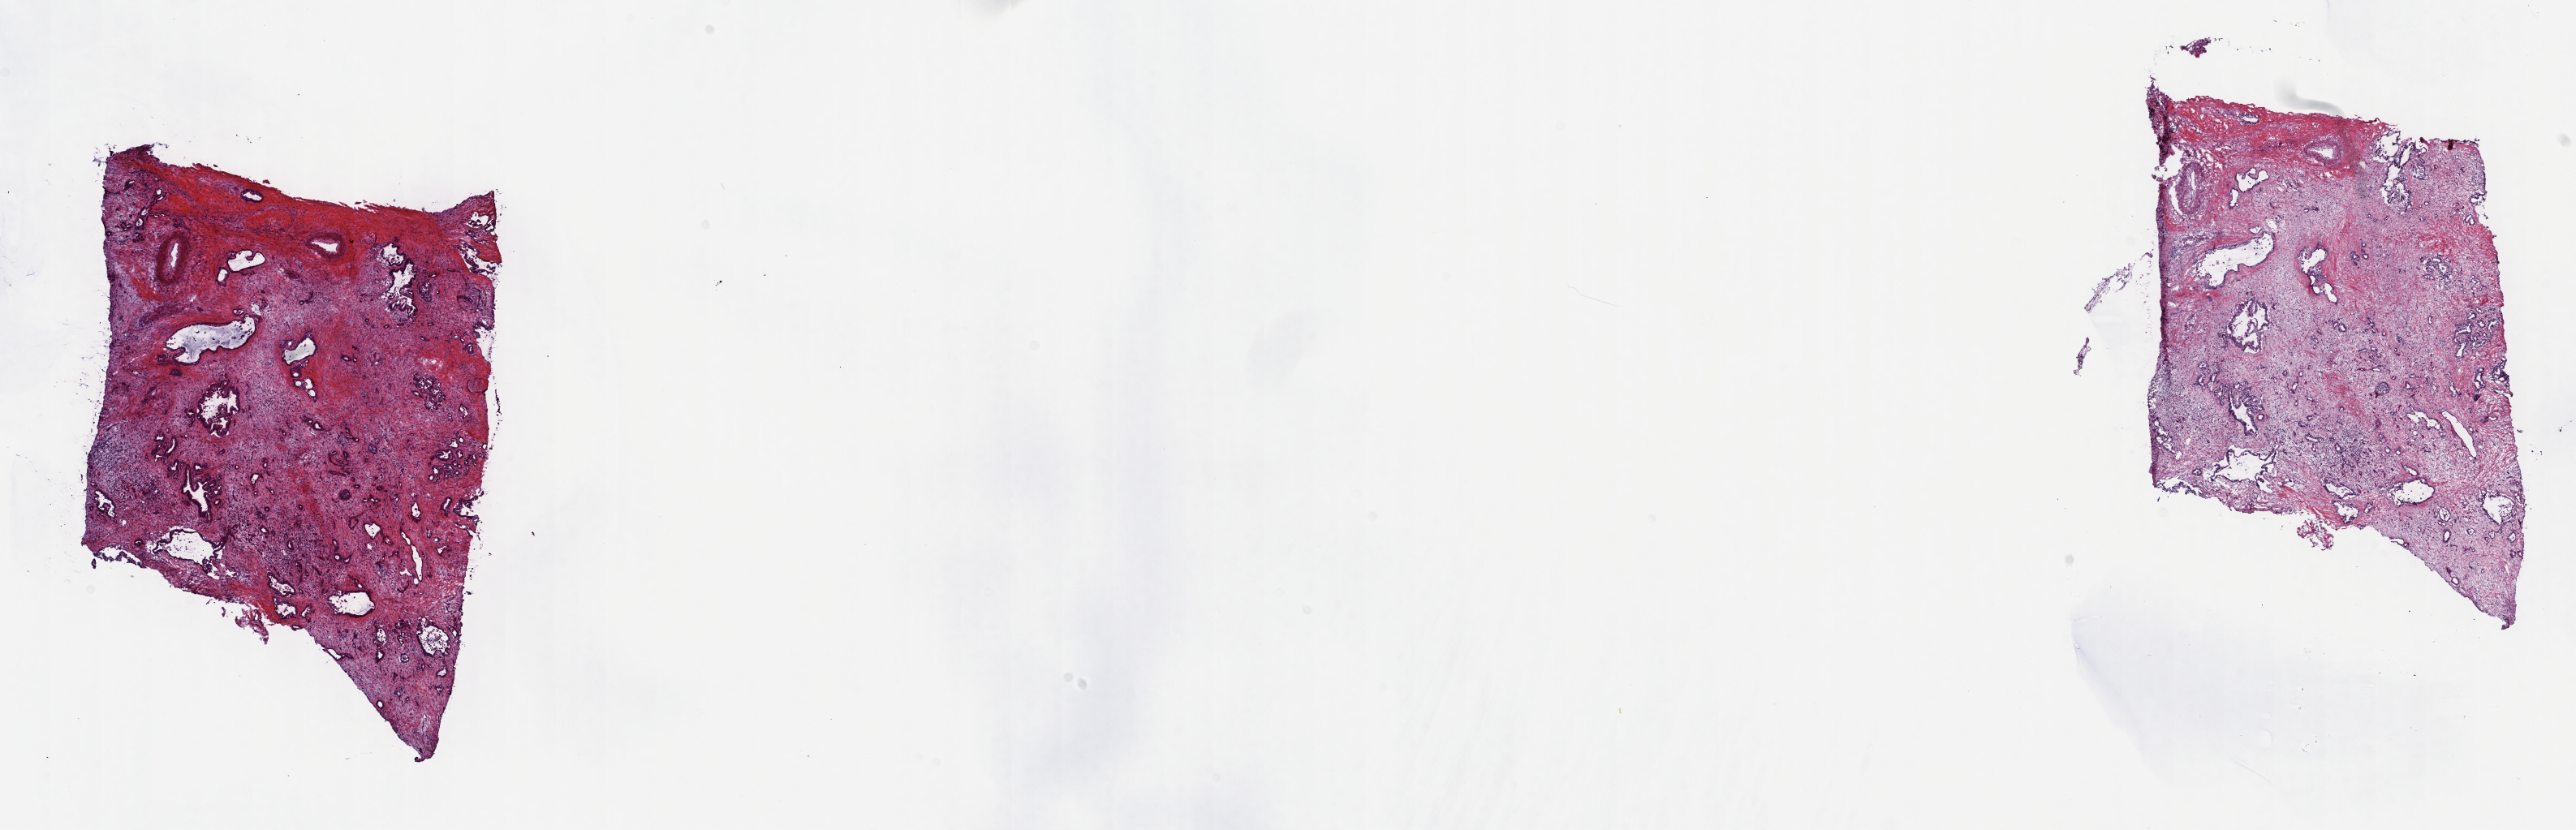
Hematoxylin and eosin (H&E) stained whole-slide image — shown as a low-resolution overview of the whole scanned area (about 25.7 x 8.3 mm, acquisition: 40x scan); frozen section from the top of the tissue portion; pancreas, primary tumour sample. Male patient; age at initial diagnosis 70 years. Pathologist review of this section (percent, as recorded): tumour cells 100%, tumour nuclei 20%.
Histologic diagnosis: Adenocarcinoma, NOS.